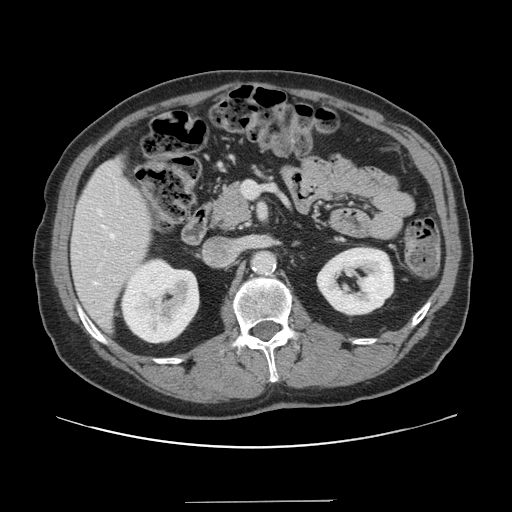
Contrast-enhanced abdominal CT, one axial slice. Position 68 of 151 along the scan axis. Intravenous contrast given. Soft-tissue window (W 400 / L 40 HU). 2.5 mm slice thickness. 512 × 512 image matrix. Male patient, age 63 years. Case-level facts recorded for this patient, not image findings: diagnosis: colorectal cancer liver metastases, imaged before liver resection; multiple liver metastases: no.
Annotated regions visible in this slice (expert manual segmentation):
- hepatic veins: bounding box <94,210,115,285> (left, top, right, bottom; pixels)
- liver: <73,159,151,329>
- planned liver remnant (the part of the liver to remain after resection): <72,160,152,330>
- portal vein (with intrahepatic branches): <104,181,258,254>